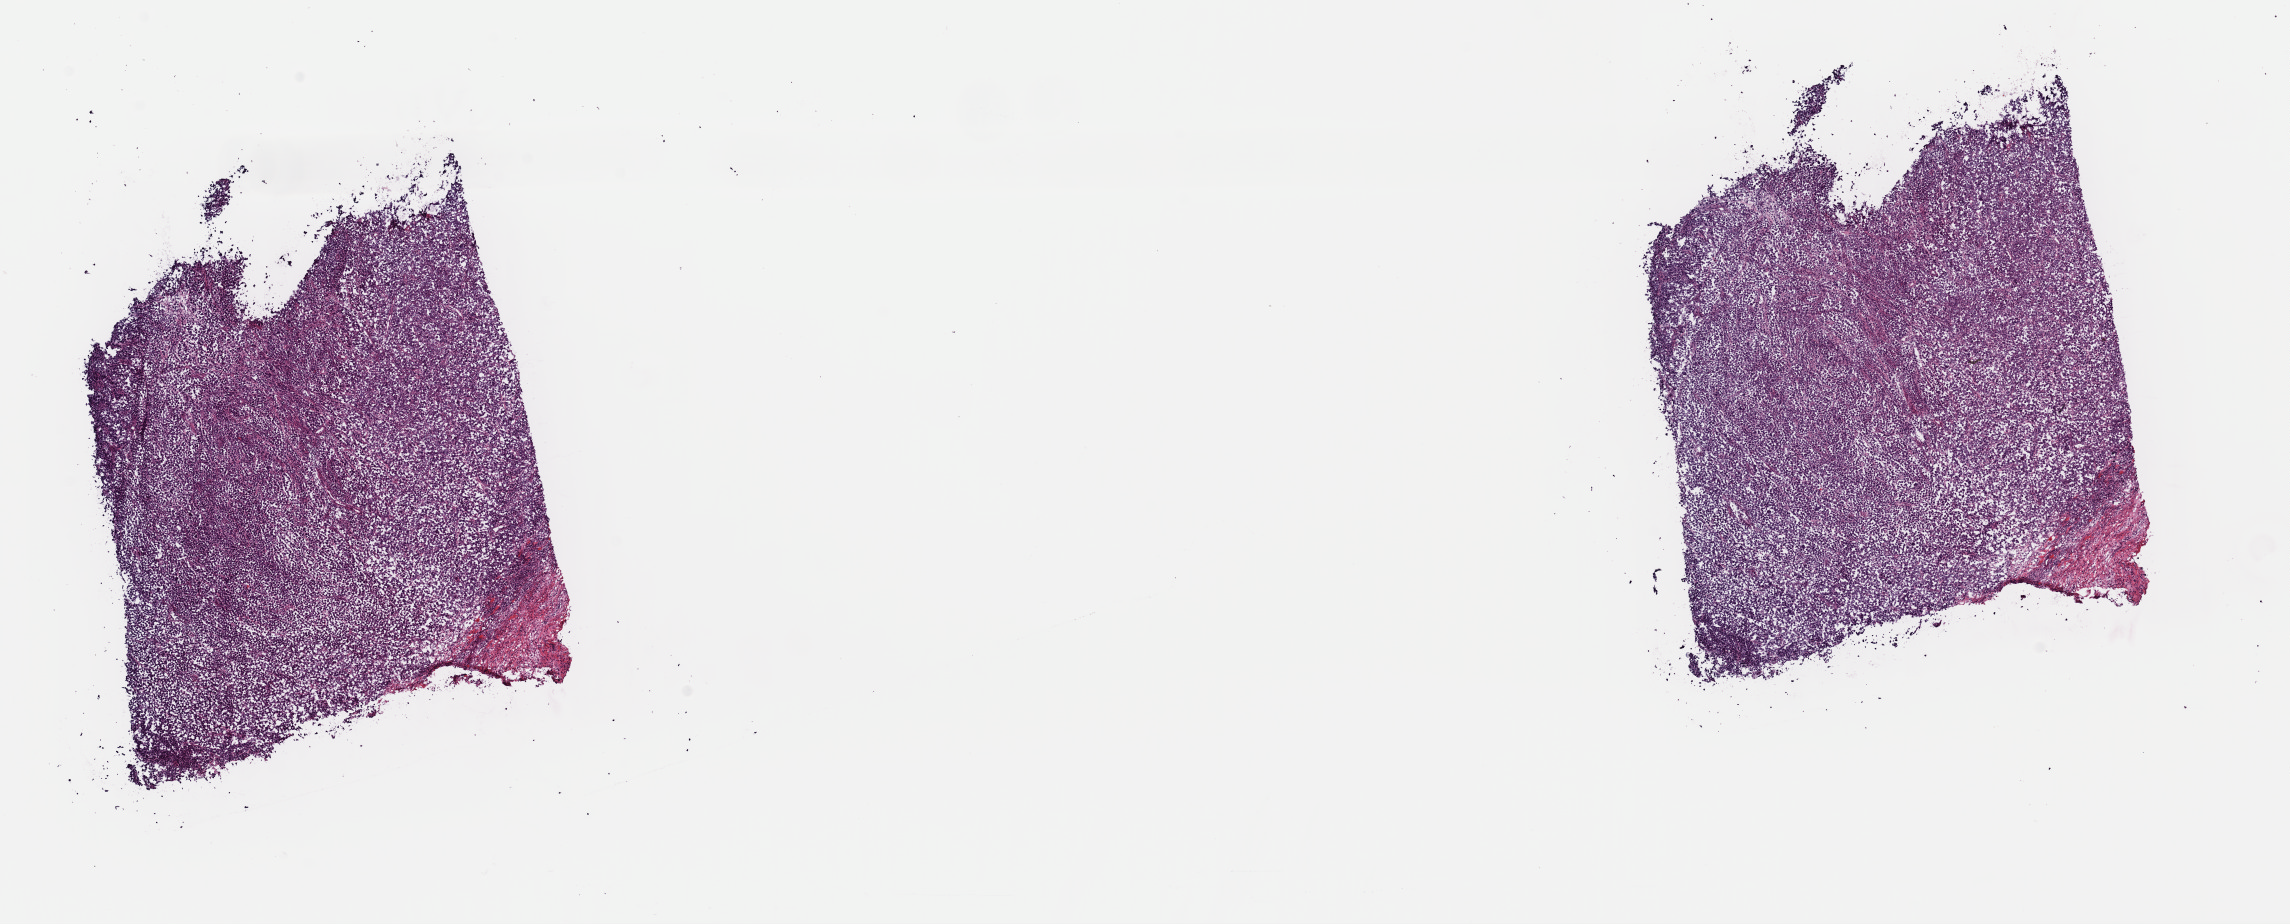
Digitized Hematoxylin and eosin (H&E) stained tissue section (whole slide), a low-resolution overview of the entire scanned area, about 18.1 x 7.3 mm (from a 40x scan); frozen section; metastatic tumour sample. Patient: male, age at initial diagnosis 45 years. Composition of this section per pathologist review: tumour cells 80%, tumour nuclei 80%, normal cells 0%, stromal cells 20%, necrosis 0%. Infiltration values recorded for this section: lymphocyte infiltration 5%, monocyte infiltration 0%, neutrophil infiltration 3%.
- this section: metastatic tumour tissue
- patient diagnosis: Malignant melanoma, NOS